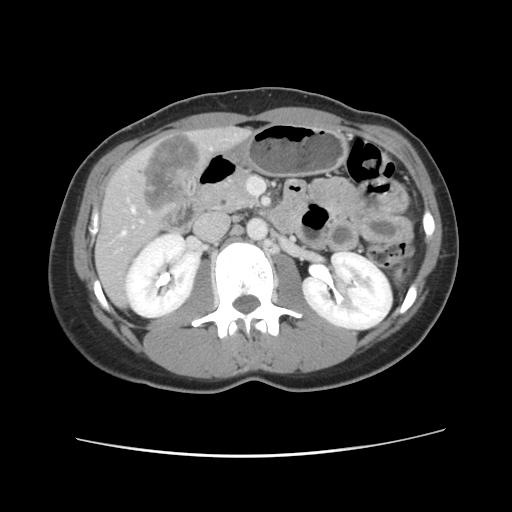
Contrast-enhanced abdominal CT, one axial slice. Slice 41 of 134 in the series (ordered by position). Intravenous contrast given. Soft-tissue window (W 400 / L 40 HU). 512 × 512 image matrix. Female patient, age 33 years. From the clinical record (not read from this slice): diagnosis: colorectal cancer liver metastases, imaged before liver resection; multiple liver metastases: yes; largest metastasis: 4.5 cm; disease in both lobes: yes.
Annotated regions visible in this slice (expert manual segmentation):
- hepatic veins: bounding box <121,207,135,236> (left, top, right, bottom; pixels)
- liver: <96,127,249,306>
- planned liver remnant (the part of the liver to remain after resection): <95,240,130,307>
- liver metastasis: <137,134,200,210>